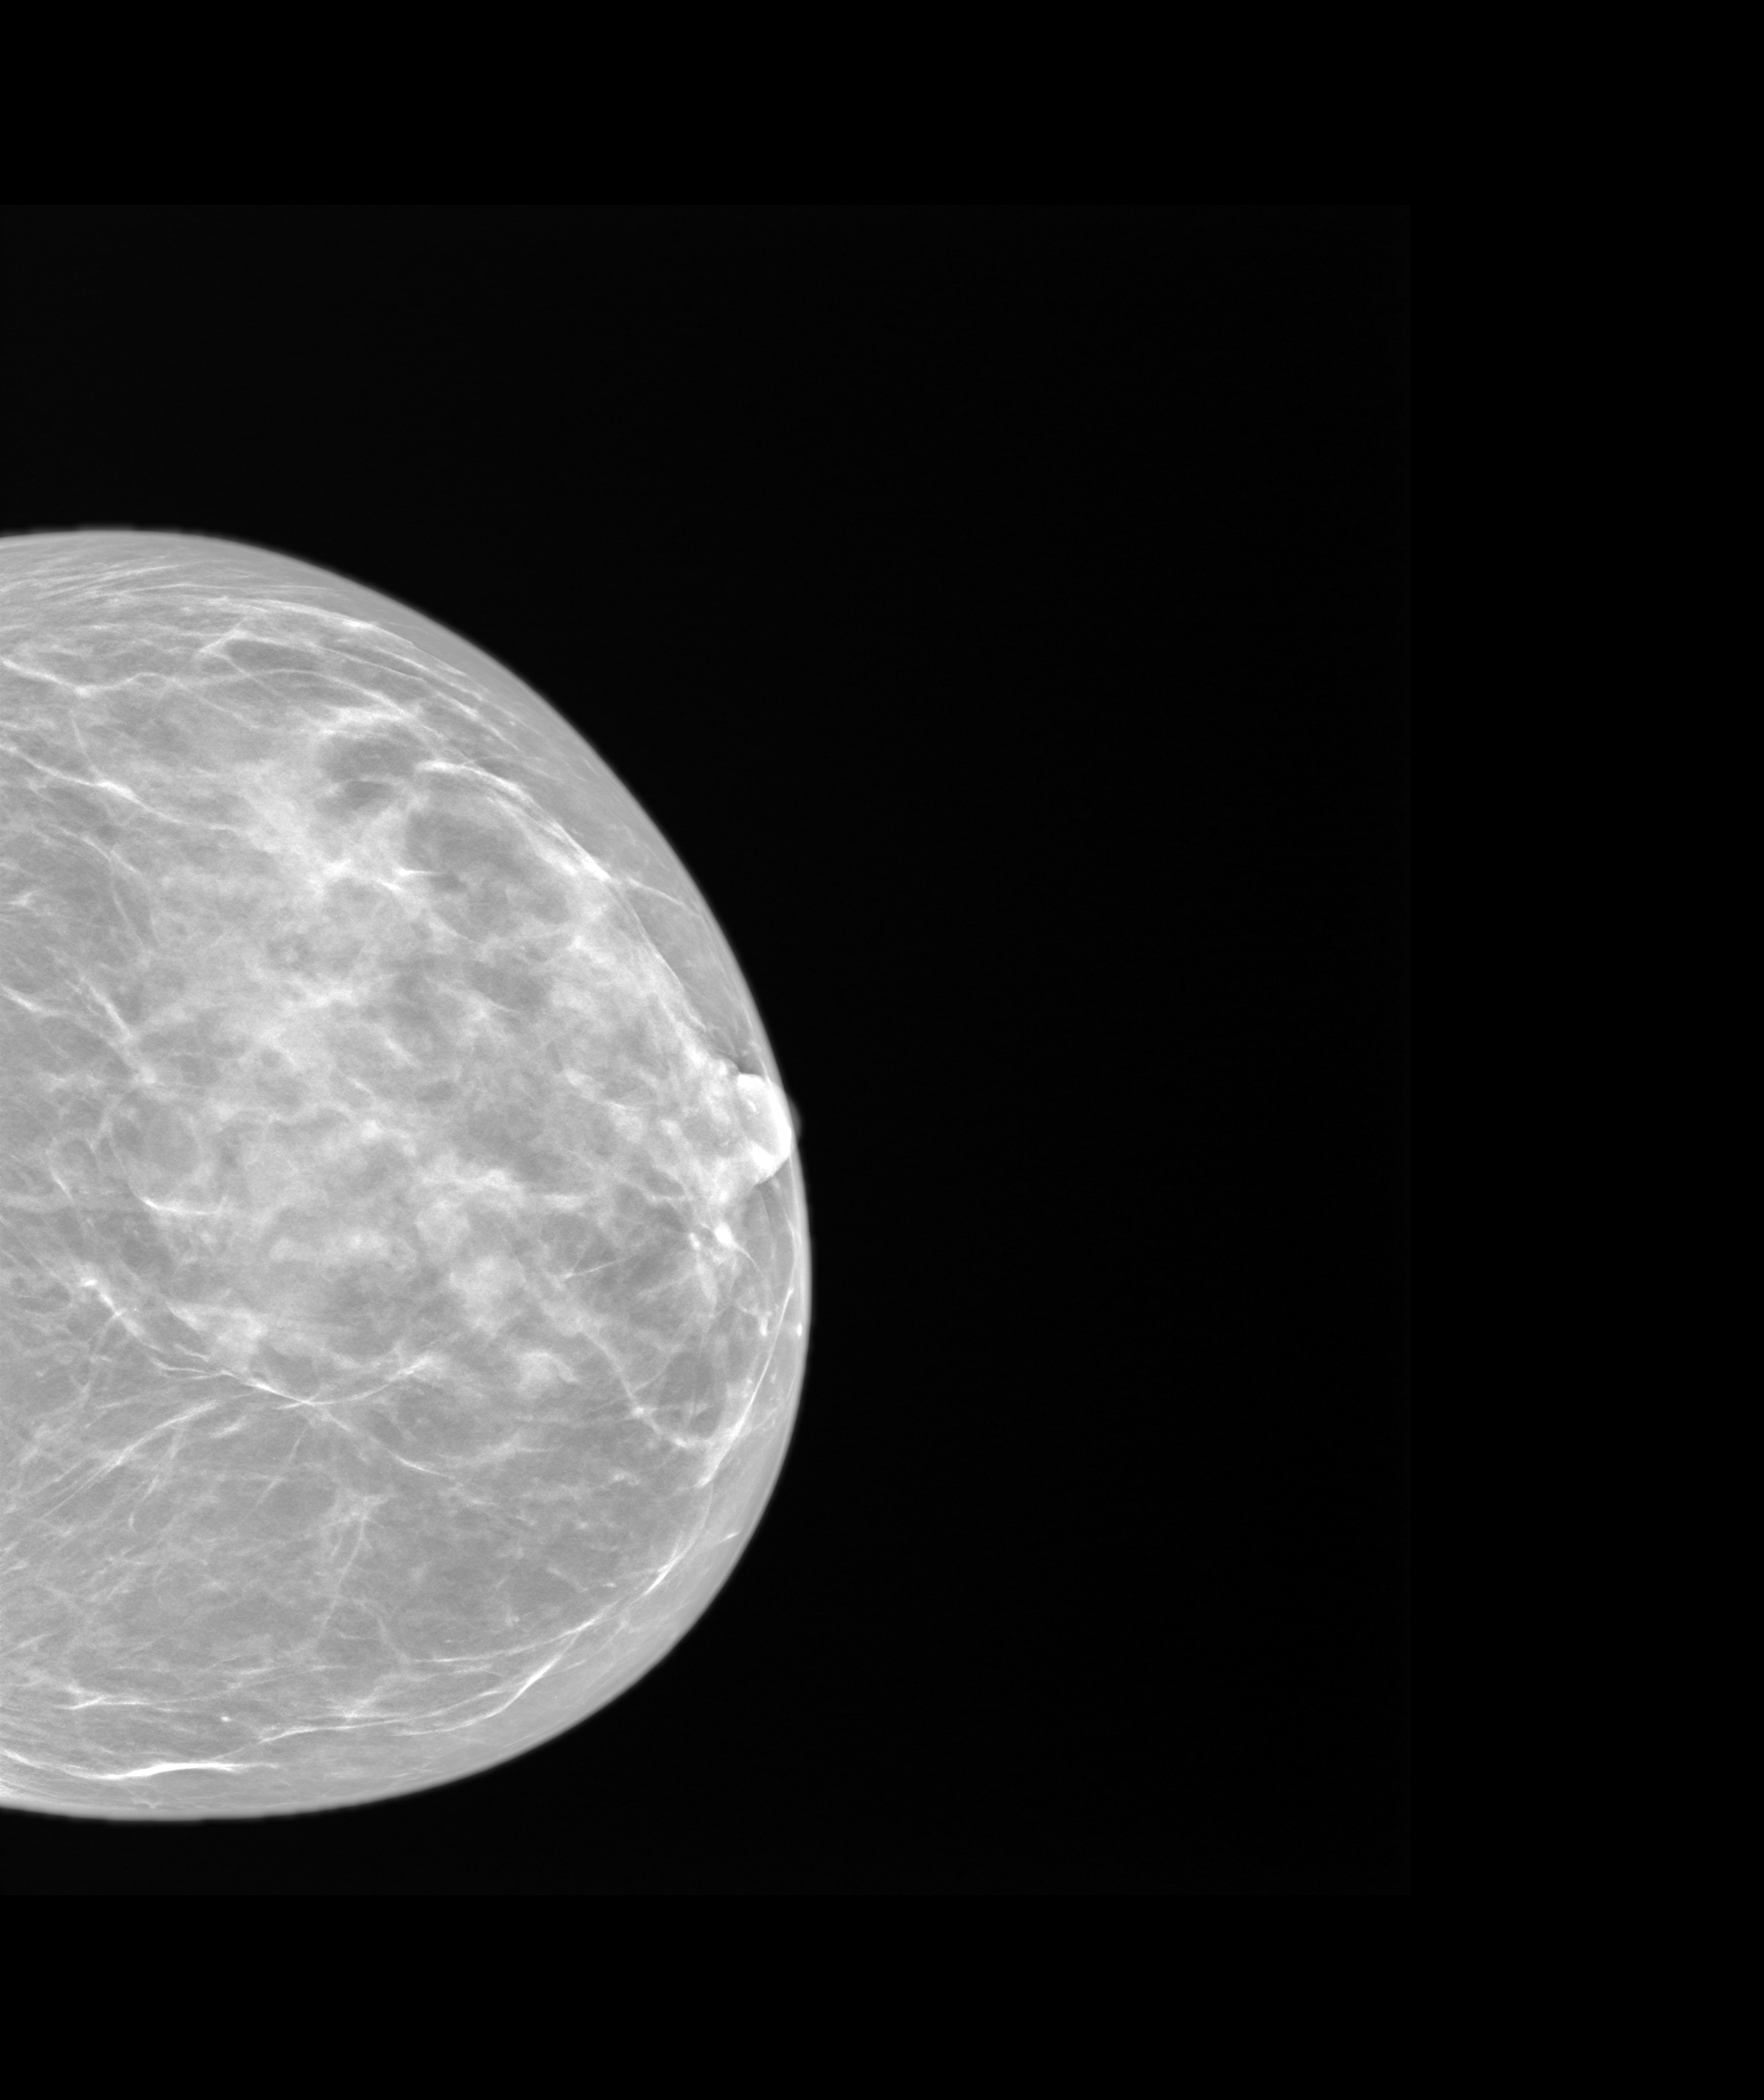
Screening examination. Female patient, age 57 years.
Image type: synthesized 2-D view from tomosynthesis. Breast: left. Projection: craniocaudal (CC) view.